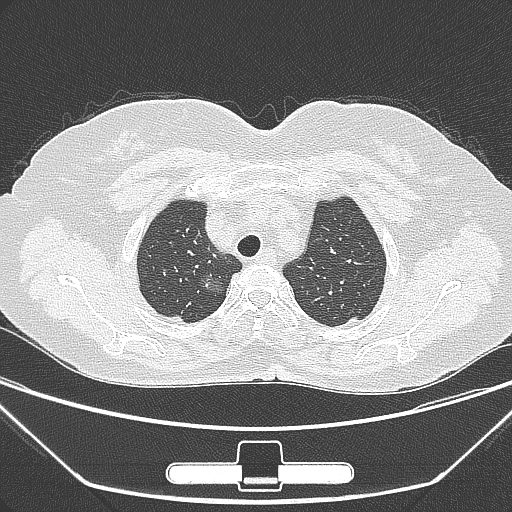
Chest CT, one axial slice; slice 233 of 275 in the series (ordered by position); 120 kVp; lung window (W 1500 / L -600 HU); 512 × 512 image matrix, field of view 356 × 356 mm. Patient: female, 63 years. From the clinical record (not read from this slice): clinical TNM (as recorded): T1a N0 M0; histopathological grade: G1.
Outlined on this slice (bounding box drawn by a radiologist):
- lung tumour (recorded histology: adenocarcinoma): bounding box <191,274,232,308> (left, top, right, bottom; pixels)